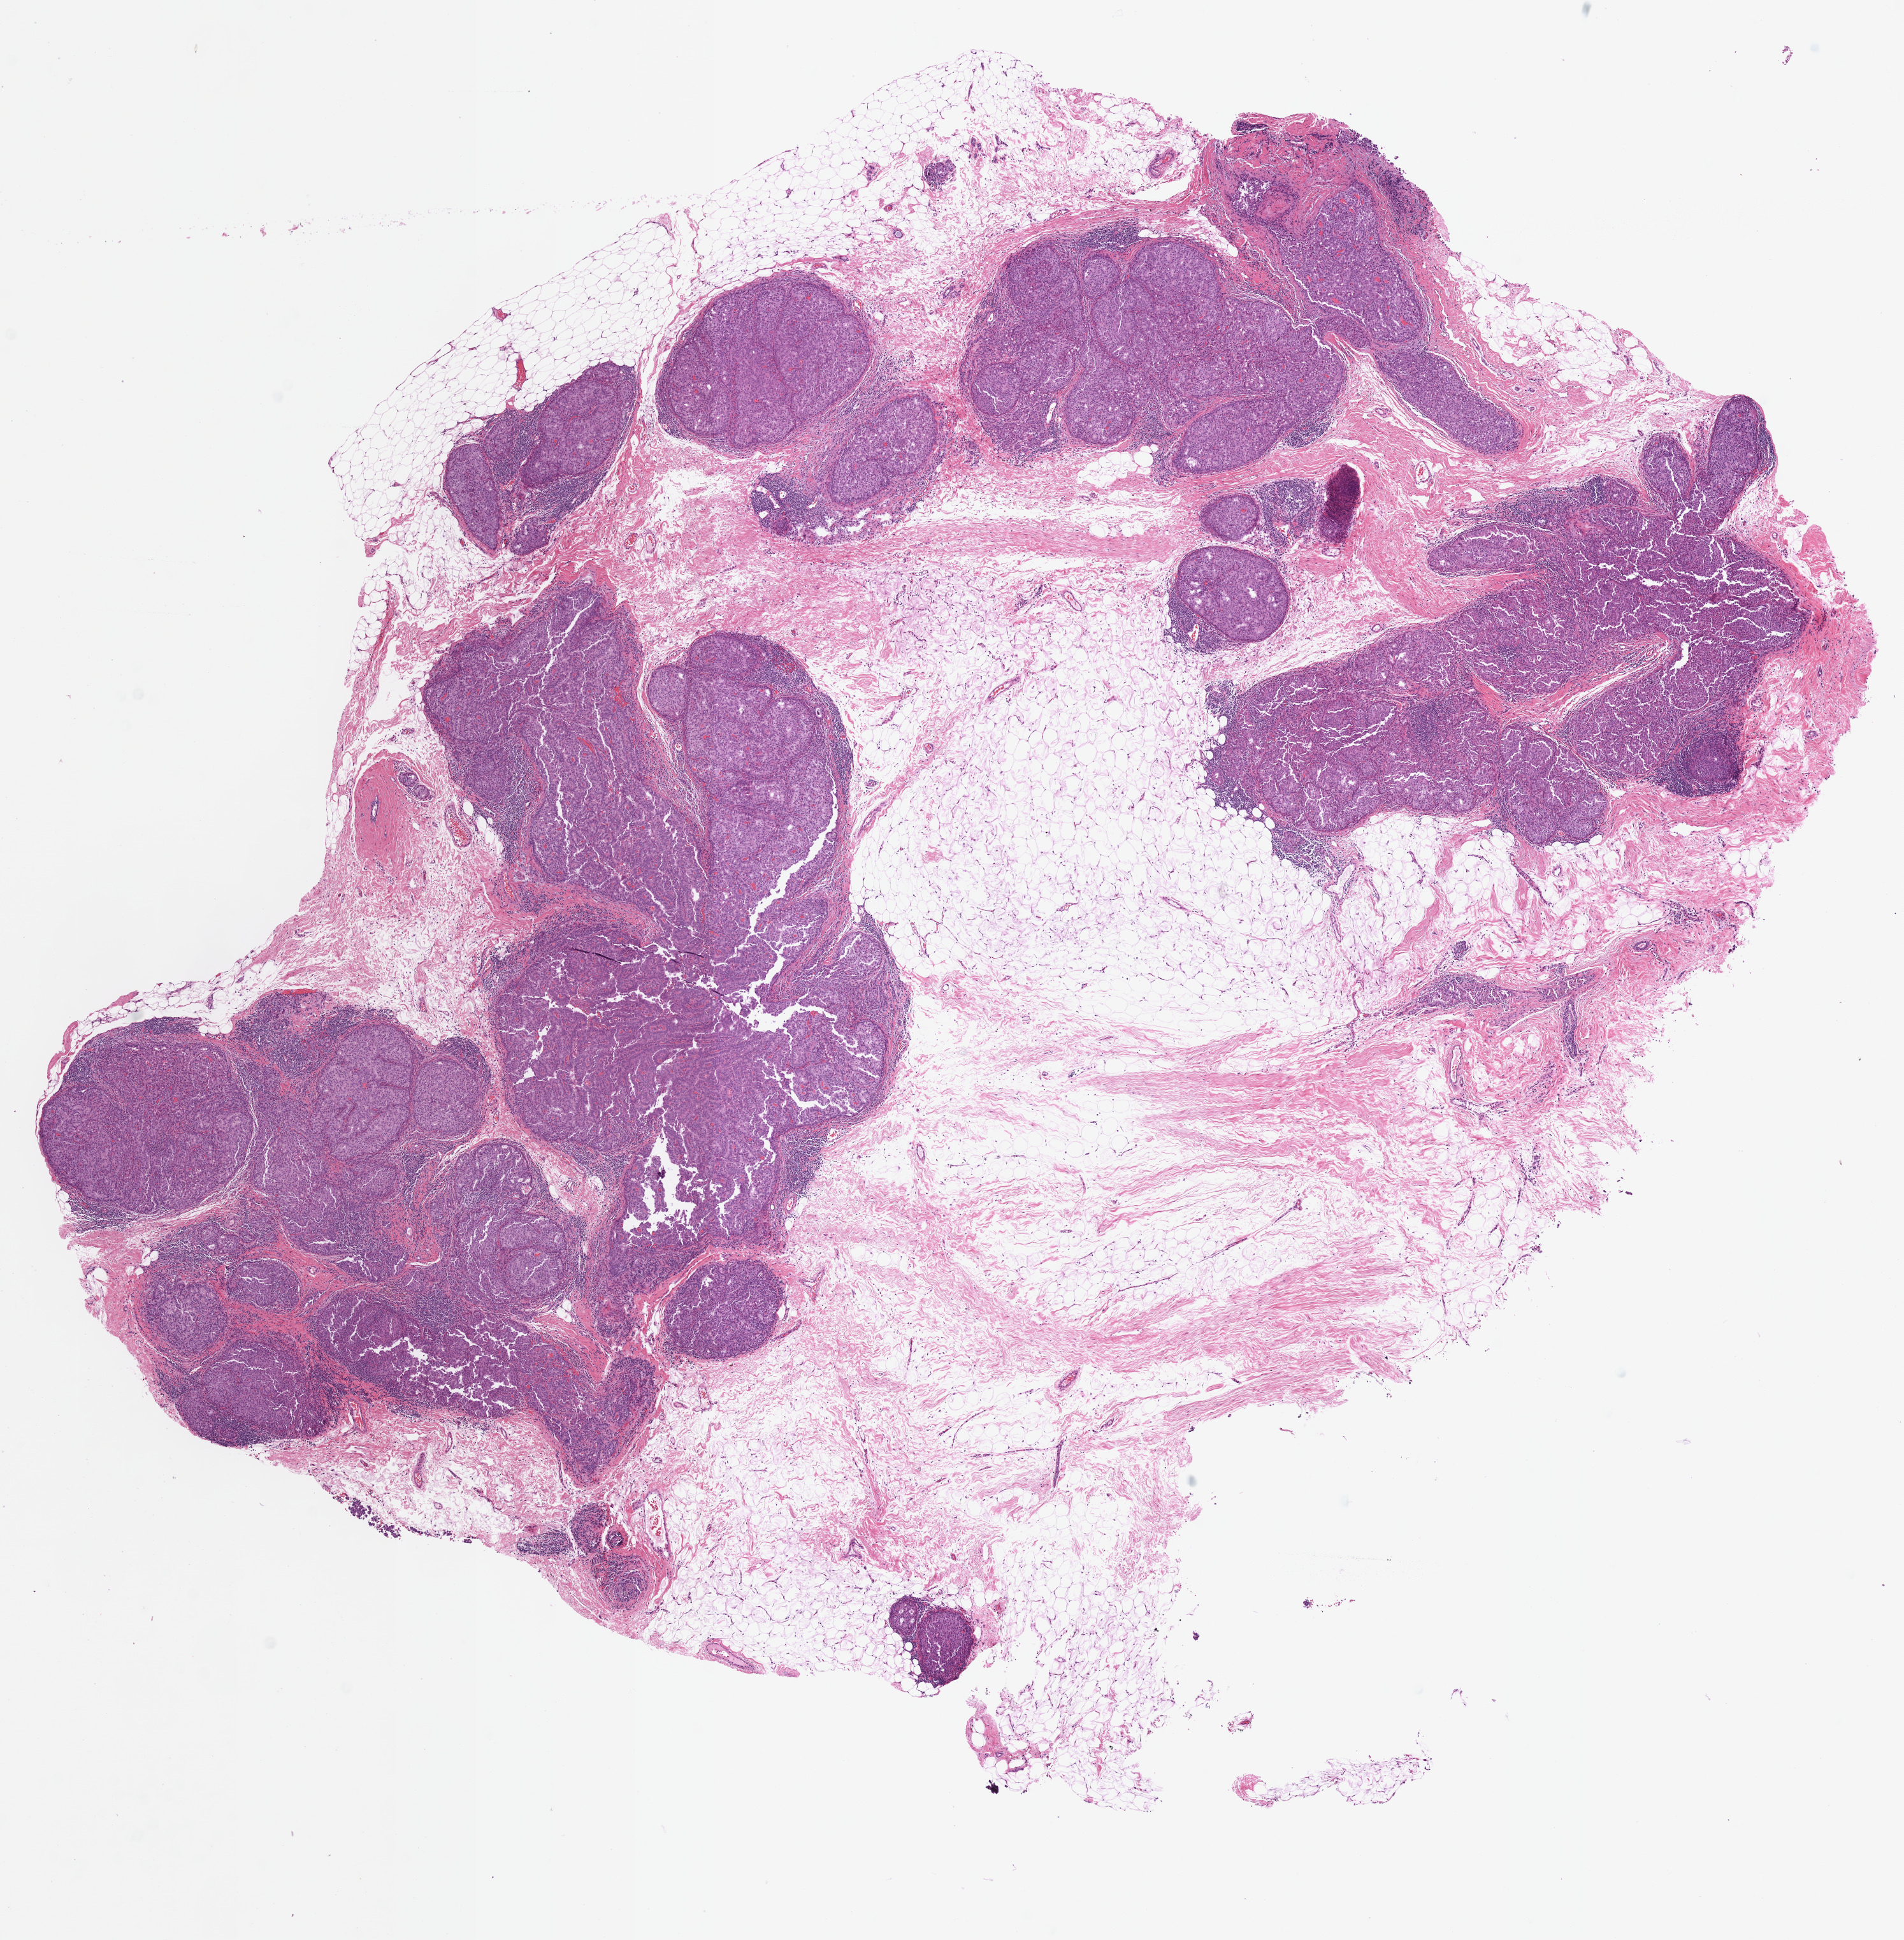
H&E whole-slide image — whole scanned area (about 11.7 x 12.0 mm, from a 40x scan) shown as a low-resolution overview; formalin-fixed paraffin-embedded (FFPE) diagnostic section; primary tumour sample from the breast. Female, age 66 years at initial diagnosis.
Lymph nodes positive (case pathology): 0 of 1 examined. AJCC pathologic stage: IIA (7th edition). Histologic diagnosis: Papillary carcinoma, NOS.